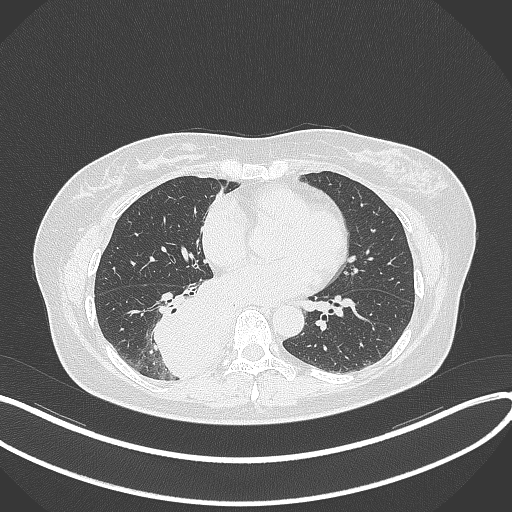
Chest CT, one axial slice. Position 154 of 331 along the scan axis. 120 kVp. Lung window (W 1500 / L -600 HU). 1 mm slice thickness. 512 × 512 image matrix, field of view 400 × 400 mm. Patient: female, 54 years. Case-level facts recorded for this patient, not image findings: clinical TNM (as recorded): T4 N0 M0.
Annotated regions visible in this slice (rectangle marked by the reading radiologist):
- lung tumour (recorded histology: adenocarcinoma): bounding box [x1, y1, x2, y2] px = [157, 279, 230, 382]